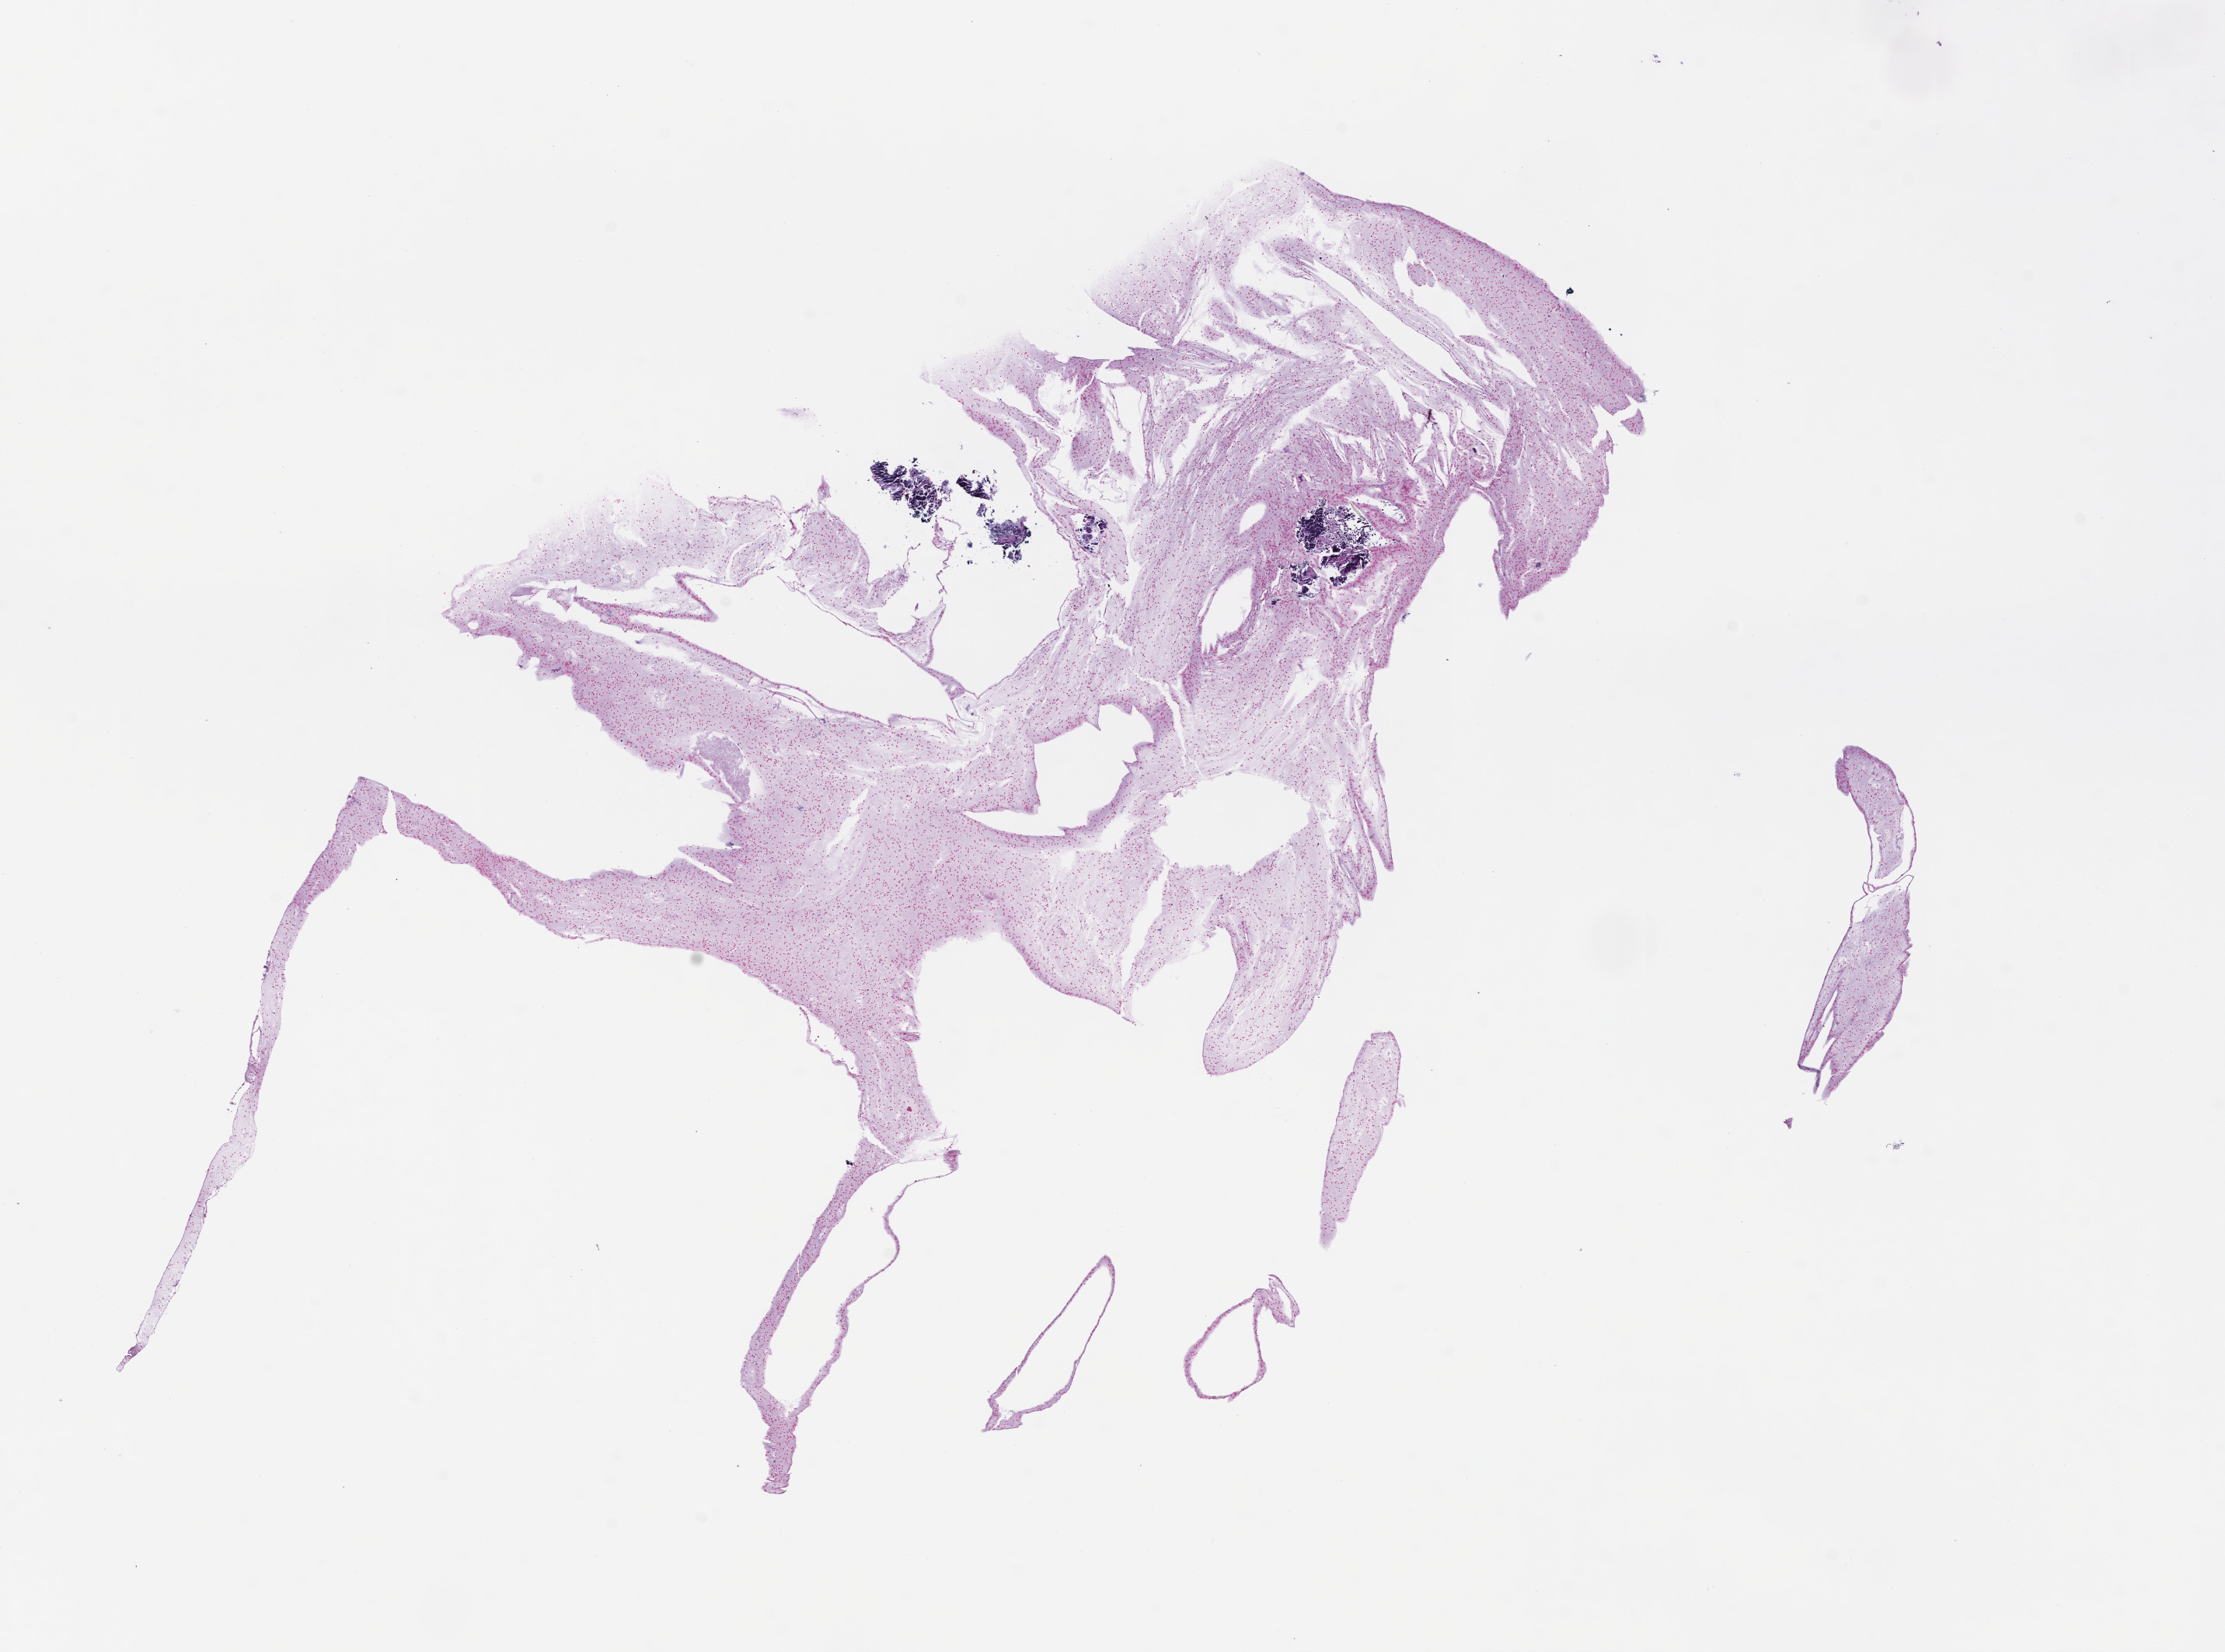
Digitized haematoxylin and eosin-stained section — shown as a low-resolution overview of the whole scanned area (about 11.6 x 8.6 mm). Formalin-fixed paraffin-embedded section. Site: lung. Male patient.
This section: primary tumour tissue. Diagnosis: Small Cell Lung Carcinoma.